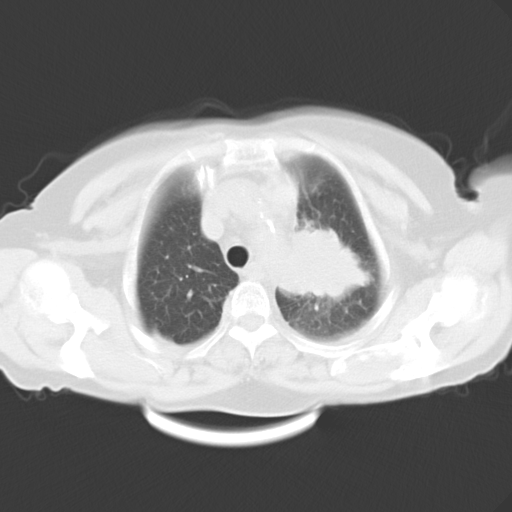
Chest CT, one axial slice; position 22 of 26 along the scan axis; reconstruction kernel B40f; 120 kVp; lung window (W 1500 / L -600 HU); 10 mm slice thickness; 512 × 512 image matrix. Patient: female, 71 years. Case-level facts recorded for this patient, not image findings: clinical TNM (as recorded): T3 N3 M0.
Outlined on this slice (bounding box drawn by a radiologist):
- lung tumour (recorded histology: adenocarcinoma): bounding box (x1, y1, x2, y2) in pixels: (275, 221, 381, 317)